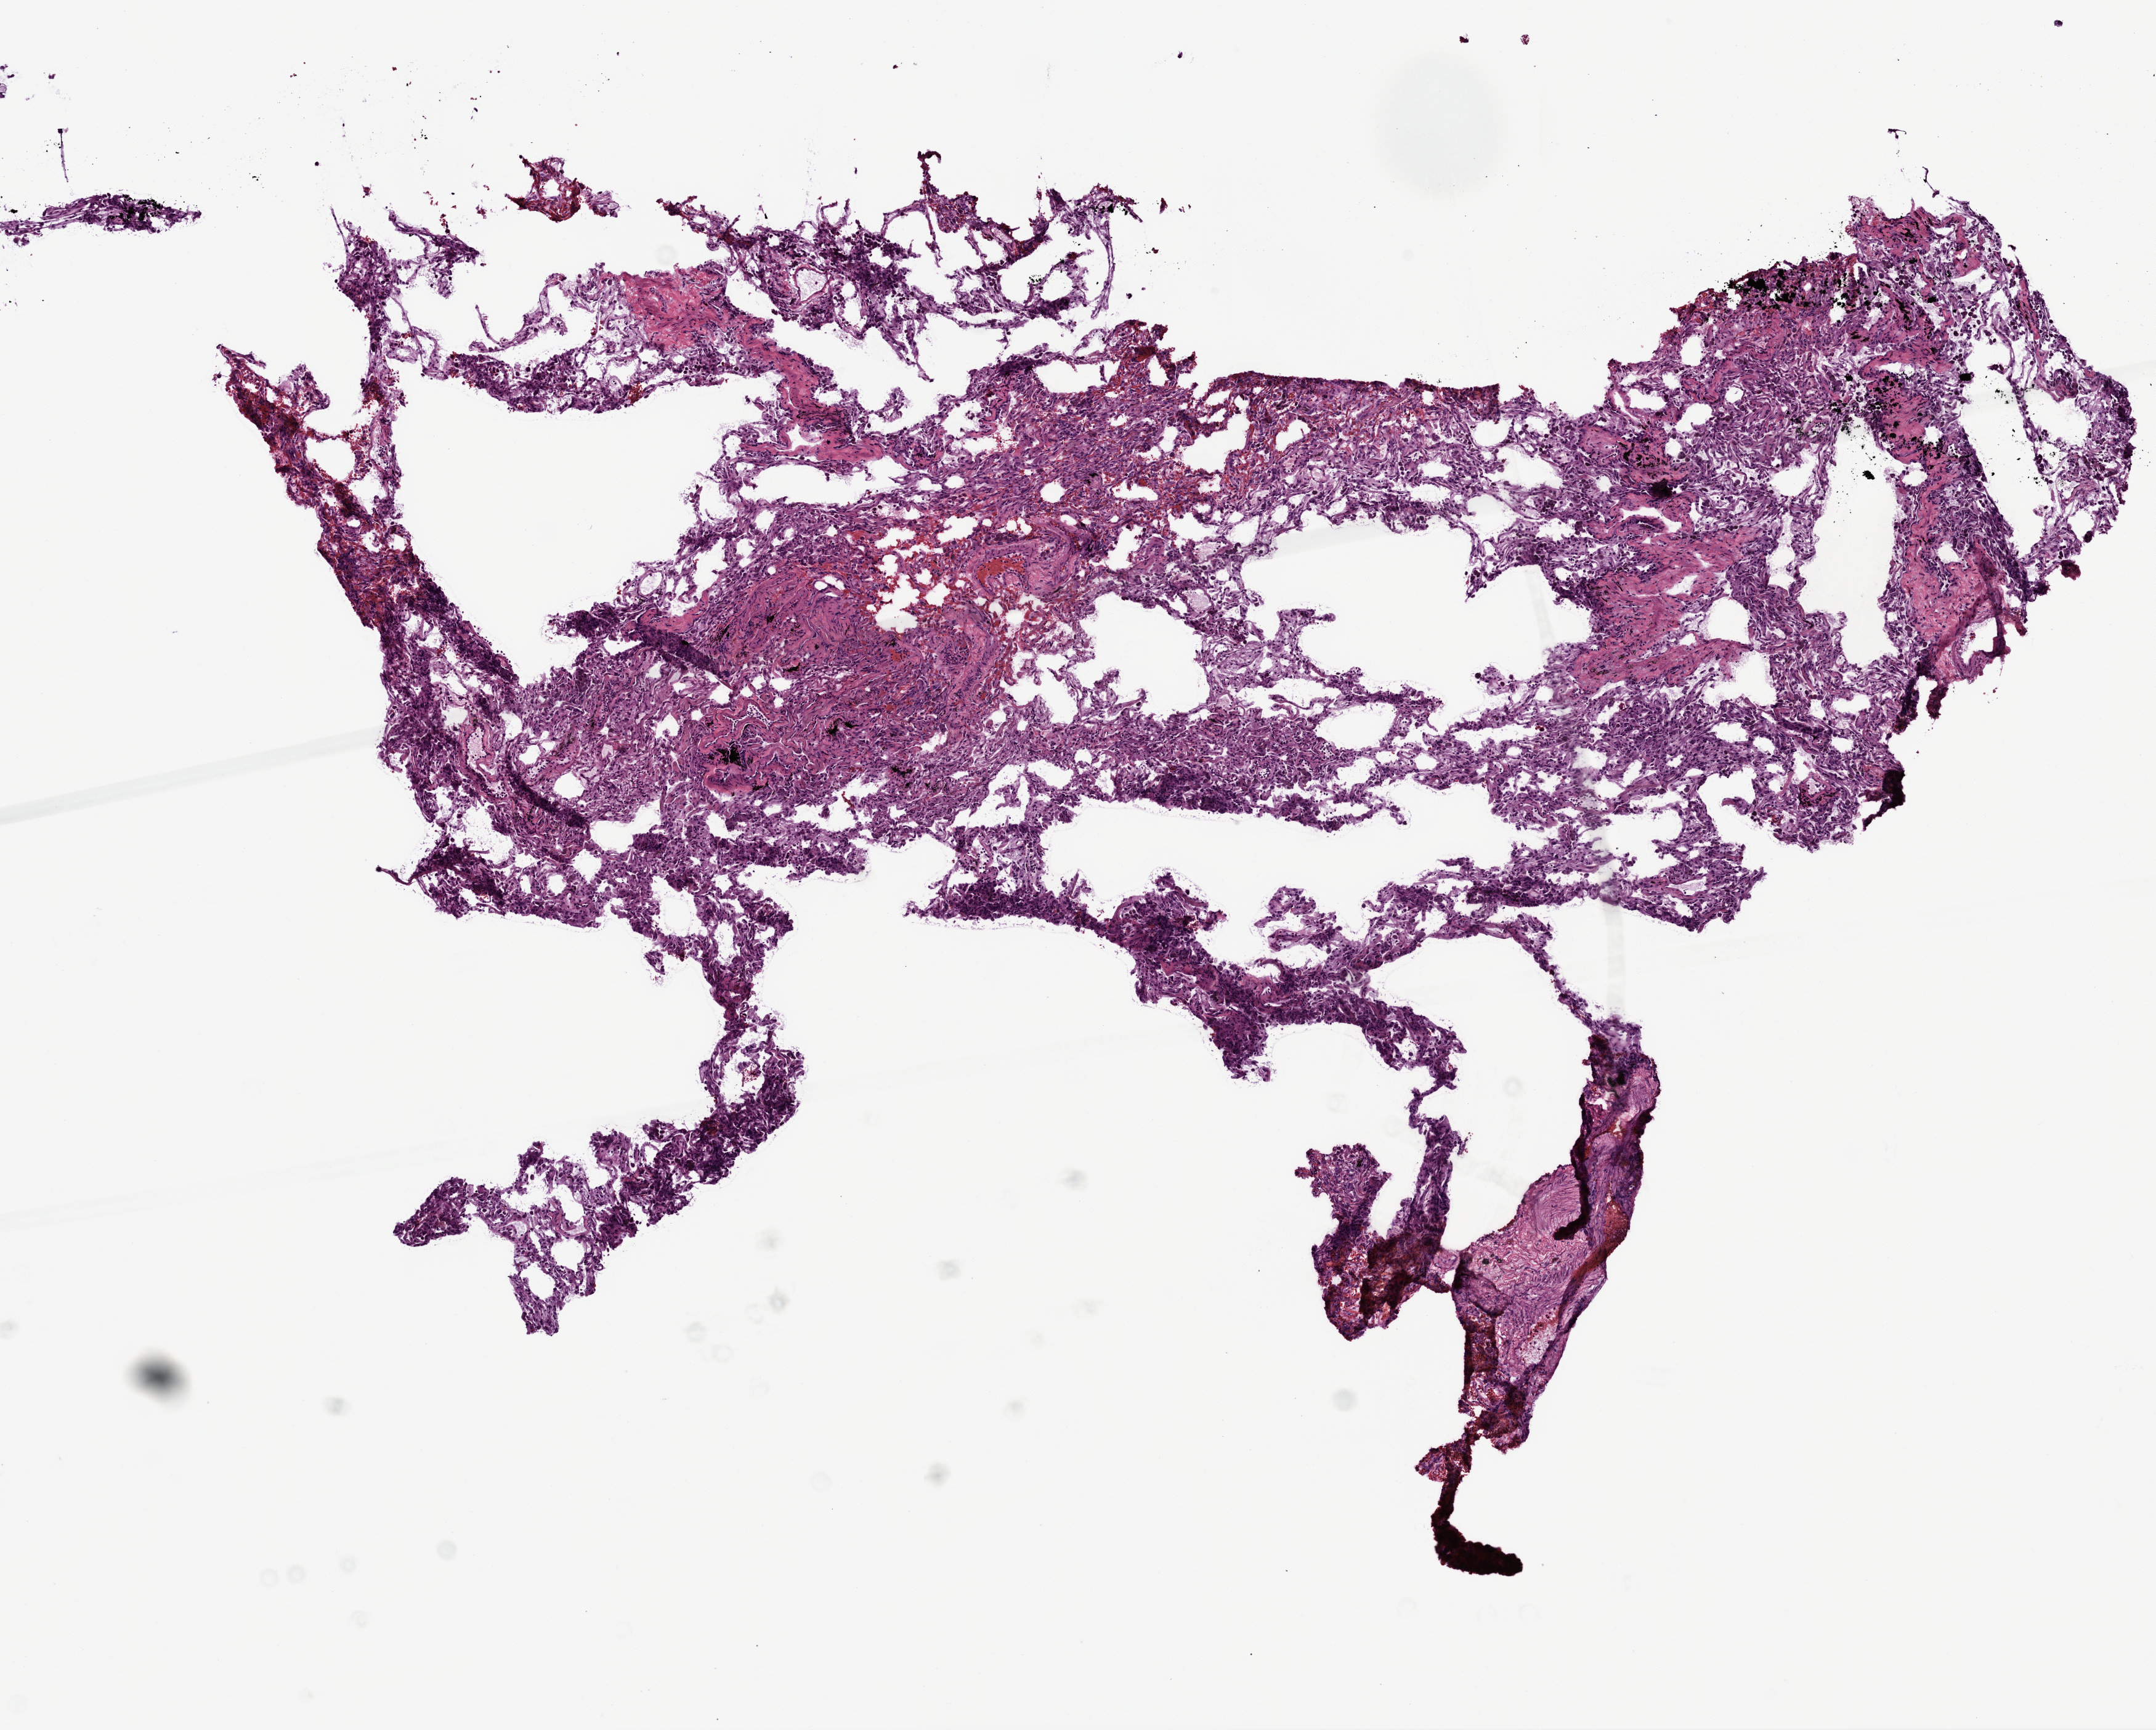
Digitized H&E-stained tissue section (whole slide), low-resolution overview of the scanned area, about 7.0 x 5.6 mm. Frozen section from the top of the tissue portion. Sample: solid tissue normal (non-tumour tissue), lung. Male, age 51 years at initial diagnosis.
* this section: solid tissue normal sample (biorepository sample class)
* patient diagnosis: Squamous cell carcinoma, NOS (upper lobe, lung)